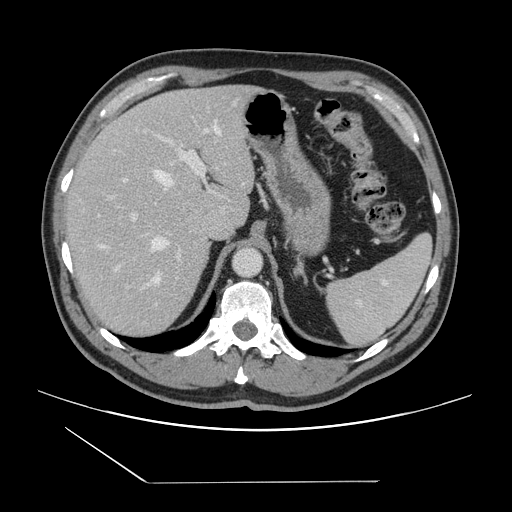
Contrast-enhanced abdominal CT, one axial slice. Slice 103 of 157 in the series (ordered by position). Intravenous contrast given. Soft-tissue window (W 400 / L 40 HU). 2.5 mm slice thickness. 512 × 512 image matrix, field of view 407 × 407 mm. Male patient, age 61 years. Case-level facts recorded for this patient, not image findings: diagnosis: colorectal cancer liver metastases, imaged before liver resection; multiple liver metastases: yes; largest metastasis: 5.5 cm; disease in both lobes: yes.
Outlined on this slice (outlined manually by an expert reader):
- hepatic veins: box from (x=152, y=126) to (x=220, y=283) px
- liver: (x=68, y=86)–(x=255, y=337)
- planned liver remnant (the part of the liver to remain after resection): (x=68, y=86)–(x=238, y=227)
- portal vein (with intrahepatic branches): (x=101, y=129)–(x=209, y=269)